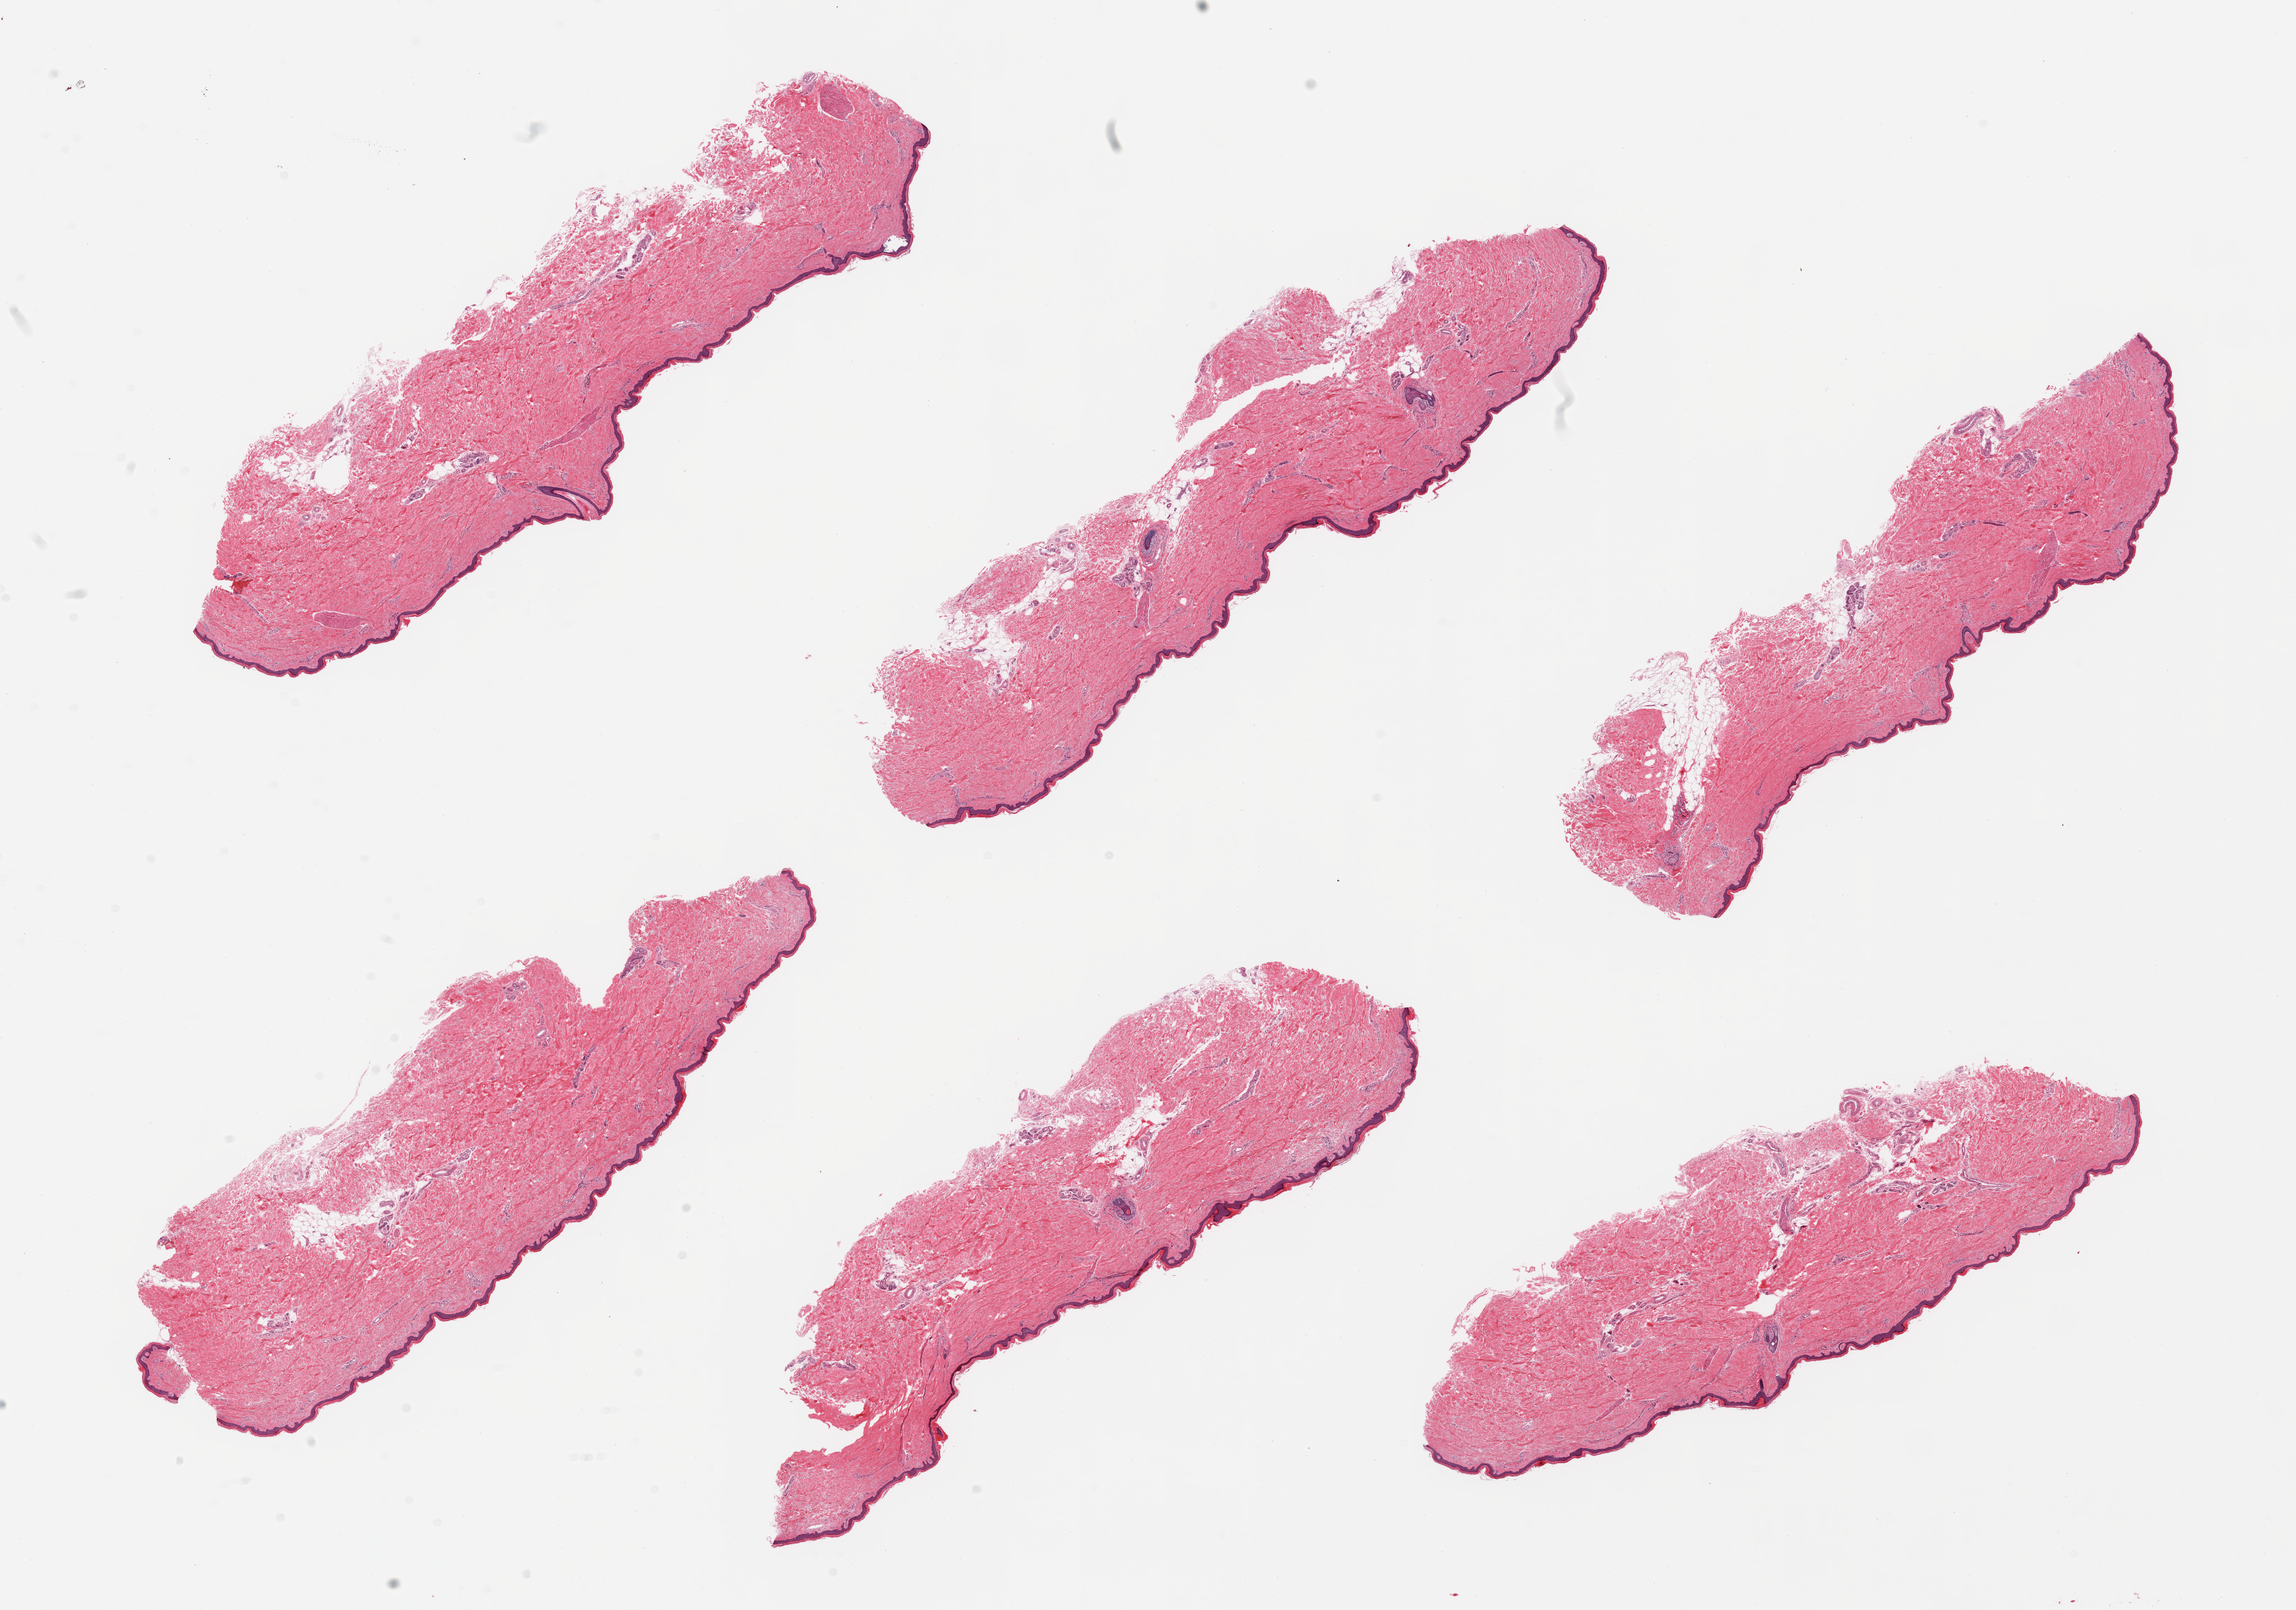
Digitized haematoxylin and eosin-stained section, brightfield — a low-resolution overview of the entire scanned area, about 25.6 x 17.9 mm; PAXgene-fixed paraffin-embedded (PFPE) section; section of skin of lower leg (target tissue); donor tissue sample. Donor: male.
* reviewer comment on this tissue sample: 6 pieces; relatively well trimmed, epidermis measures 38 microns